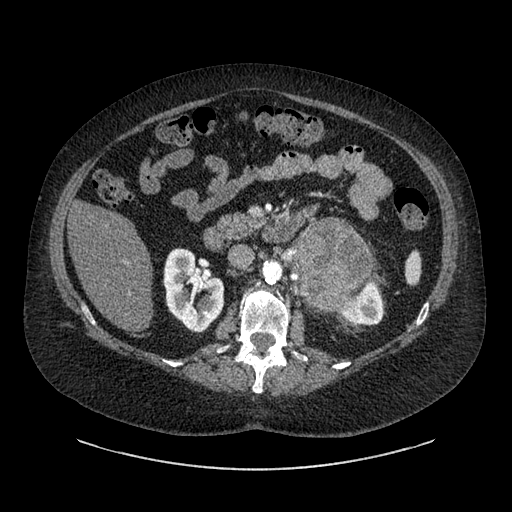
Contrast-enhanced abdominal CT, one axial slice; position 522 of 769 along the scan axis; 120 kVp; intravenous contrast given; soft-tissue window (W 400 / L 40 HU); 0.62 mm slice thickness; 512 × 512 image matrix. Female patient, age 61 years. Case-level facts recorded for this patient, not image findings: diagnosis: adrenocortical carcinoma; tumour side: left adrenal; tumour size at pathology: 13 cm; Ki-67 index: 79 %; stage (as recorded): 2.
Outlined on this slice (semi-automatically segmented with operator editing):
- mass: bounding box (x1, y1, x2, y2) in pixels: (292, 220, 374, 306)